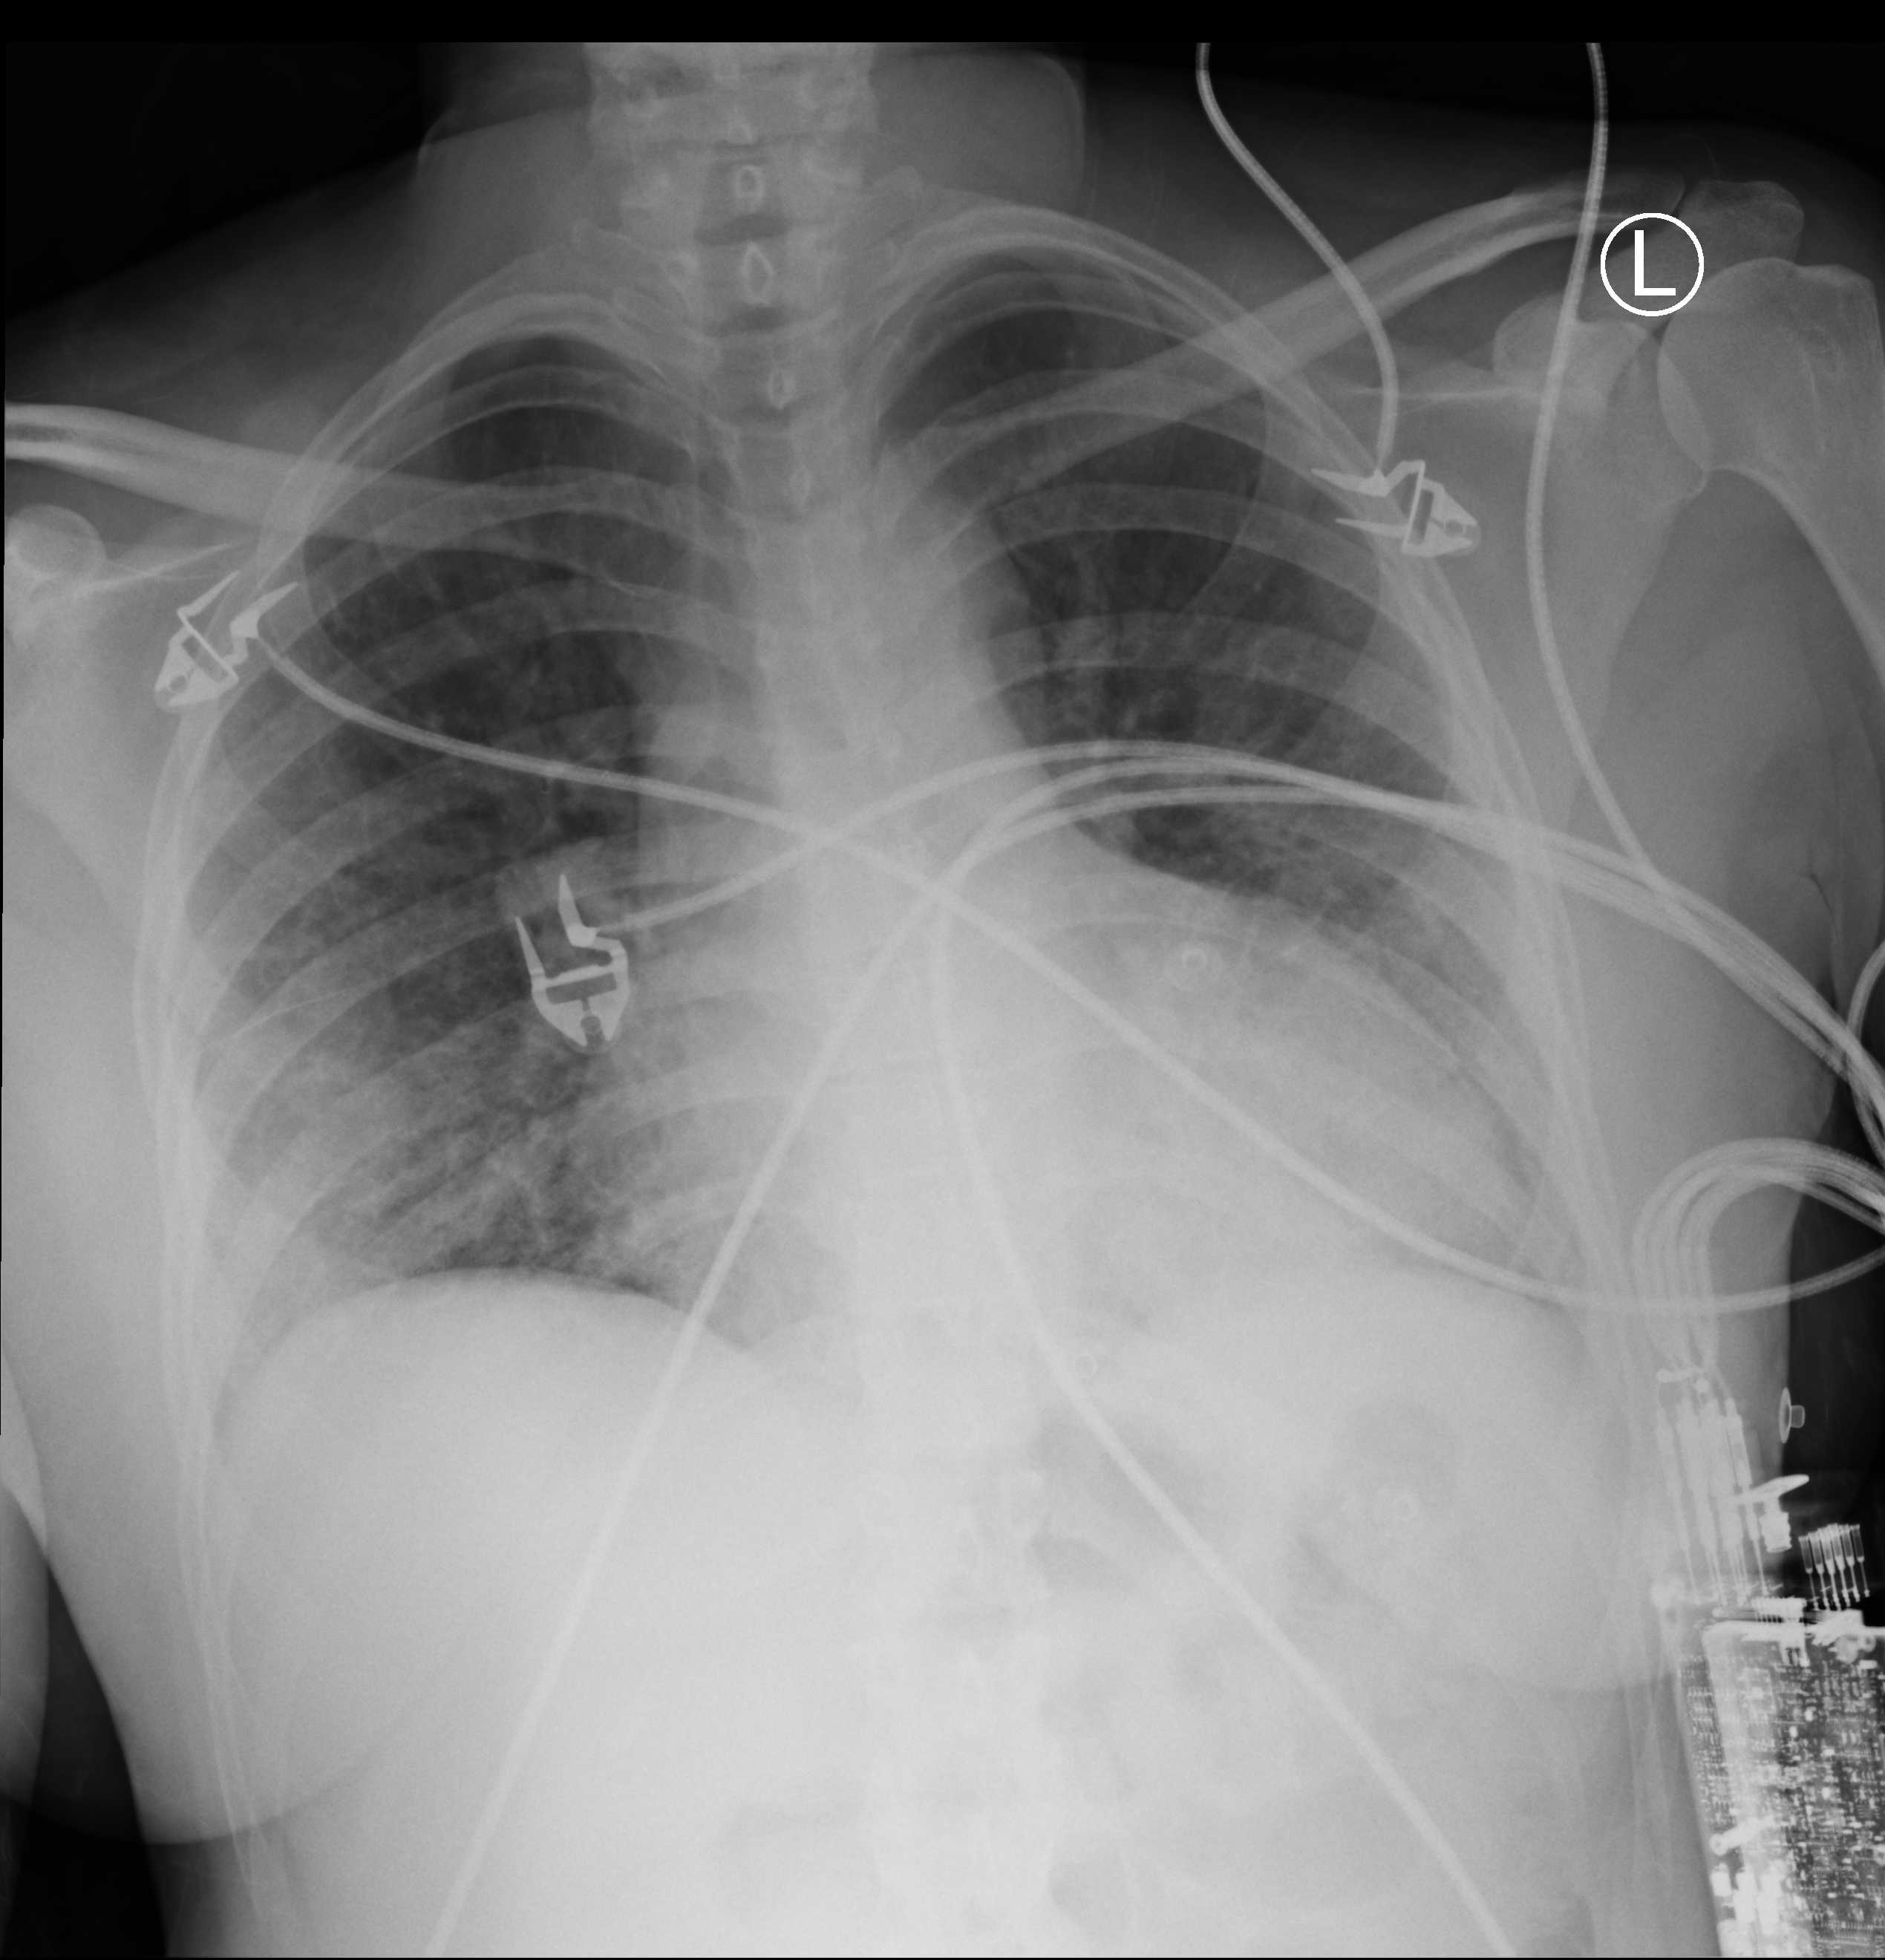
Bedside chest radiograph (computed radiography); anteroposterior (AP) projection. Patient hospitalised with COVID-19; female, aged 18–59 years.
From the hospital-stay record, not from the radiograph (when in the stay this image was taken is not recorded):
- admitted to intensive care during this hospital stay: no